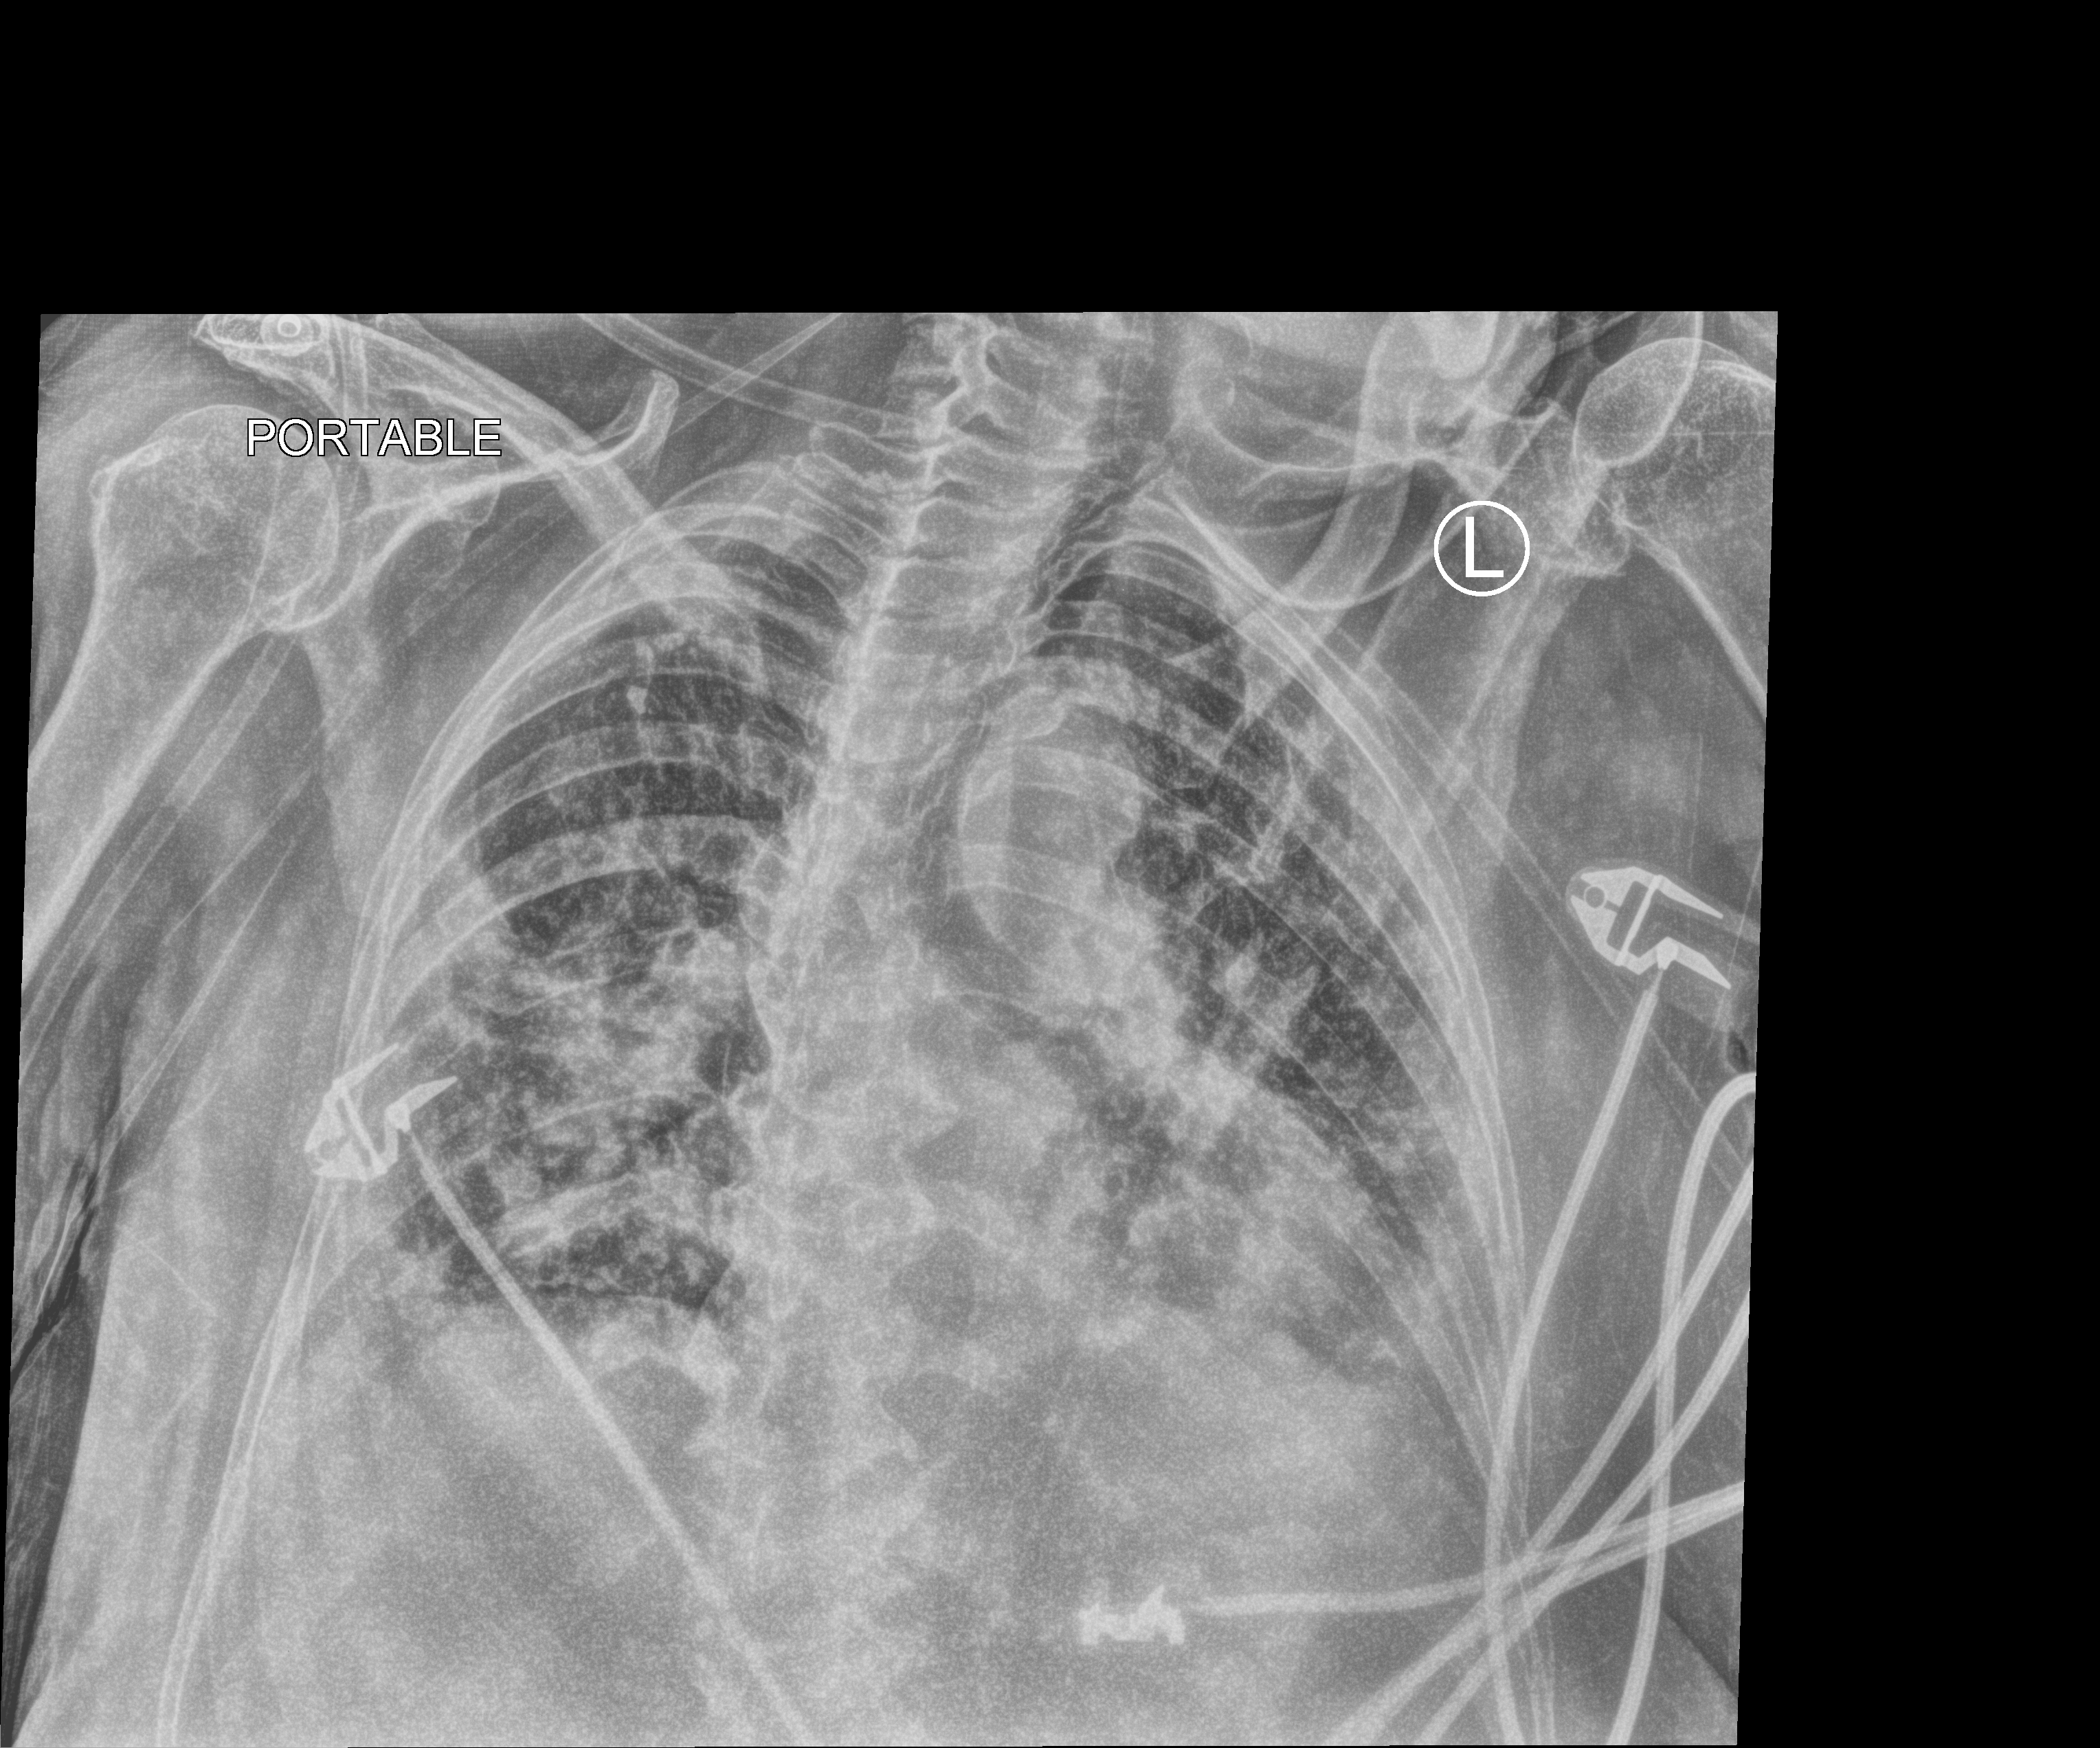
Chest X-ray (portable), anteroposterior (AP) projection. Patient hospitalised with COVID-19; female, aged 75–90 years.
Admission-level facts for this patient (not findings on this image; timing relative to this image not recorded): mechanically ventilated during this hospital stay: no; admitted to intensive care during this hospital stay: yes.